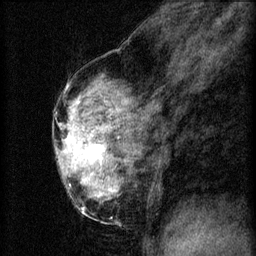
Breast MRI (dynamic contrast-enhanced), one sagittal slice. Position 34 of 60 along the scan axis. 3 images stored at this slice position (order not interpretable as contrast timing). 1.5 T. TE 4.2 ms, TR 8.2 ms. 256 × 256 image matrix, field of view 180 × 180 mm. Patient: female, 56 years.
Outlined on this slice (semi-automatic segmentation, software-assisted and operator-edited):
- analysis volume of interest (the breast-tissue region the enhancement analysis was run in; not a lesion): box from (x=60, y=124) to (x=114, y=179) px
- tumour enhancement mask (voxels above the 70 % enhancement threshold inside the analysis volume of interest): (x=65, y=128)–(x=105, y=179)